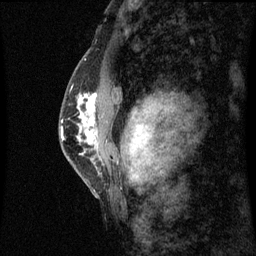
Breast MRI (dynamic contrast-enhanced), one sagittal slice; position 40 of 60 along the scan axis; dynamic contrast-enhanced series, image 2 of 3 at this slice position (ordered by acquisition); 1.5 T; TE 4.2 ms, TR 8.9 ms; 2 mm slice thickness; 256 × 256 image matrix, field of view 200 × 200 mm. Patient: female, 50 years. Case-level facts recorded for this patient, not image findings: setting: breast cancer imaged before/during neoadjuvant chemotherapy; receptor status: triple-negative.
Annotated regions visible in this slice (semi-automatically segmented with operator editing):
- analysis volume of interest (the breast-tissue region the enhancement analysis was run in; not a lesion): box from (x=68, y=80) to (x=99, y=169) px
- tumour enhancement mask (voxels above the 70 % enhancement threshold inside the analysis volume of interest): (x=82, y=96)–(x=97, y=145)